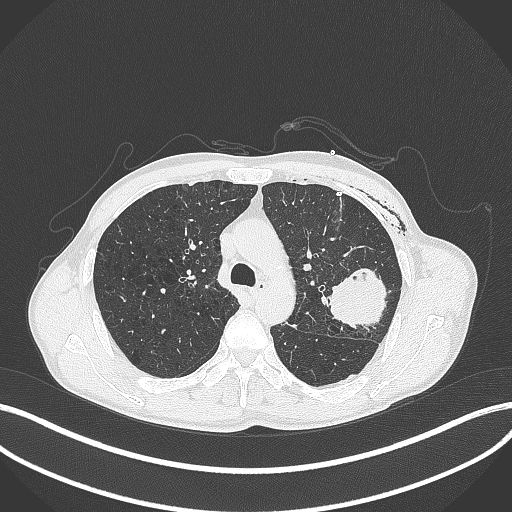
Chest CT, one axial slice; position 281 of 457 along the scan axis; reconstruction kernel B70f; 120 kVp; lung window (W 1500 / L -600 HU); 512 × 512 image matrix, field of view 400 × 400 mm. Male patient, age 58 years. Case-level facts recorded for this patient, not image findings: clinical TNM (as recorded): T3 N0 M0.
Annotated regions visible in this slice (rectangle marked by the reading radiologist):
- lung tumour (recorded histology: adenocarcinoma): bounding box <325,266,391,332> (left, top, right, bottom; pixels)